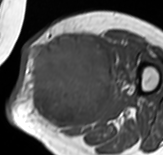
MRI of an extremity soft-tissue mass, one axial slice; position 36 of 65 along the scan axis; MR volume resampled by the dataset authors to the PET/CT grid (not the native acquisition matrix); 163 × 155 image matrix, field of view 159 × 151 mm. Female patient. From the clinical record (not read from this slice): histological type: pleomorphic leiomyosarcoma; grade: high; site of the primary tumour: left thigh.
Annotated regions visible in this slice (expert contour drawn on MRI and transferred to this co-registered scan by the dataset authors):
- gross tumour volume including surrounding oedema: bounding box <26,33,118,132> (left, top, right, bottom; pixels)
- gross tumour volume (mass): <26,33,113,130>